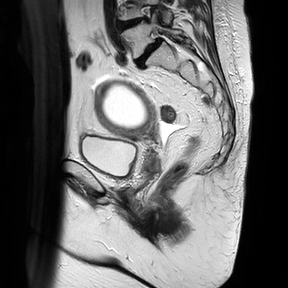
Pelvic MRI for cervical cancer, one sagittal slice. Position 20 of 30 along the scan axis. T2-weighted. 1.5 T. TE 100 ms, TR 4816.3 ms. 4 mm slice thickness. 288 × 288 image matrix, field of view 300 × 300 mm. Patient: female, 74 years.
Structures marked on this image (expert manual segmentation):
- uterus and cervix: box from (x=93, y=79) to (x=161, y=174) px